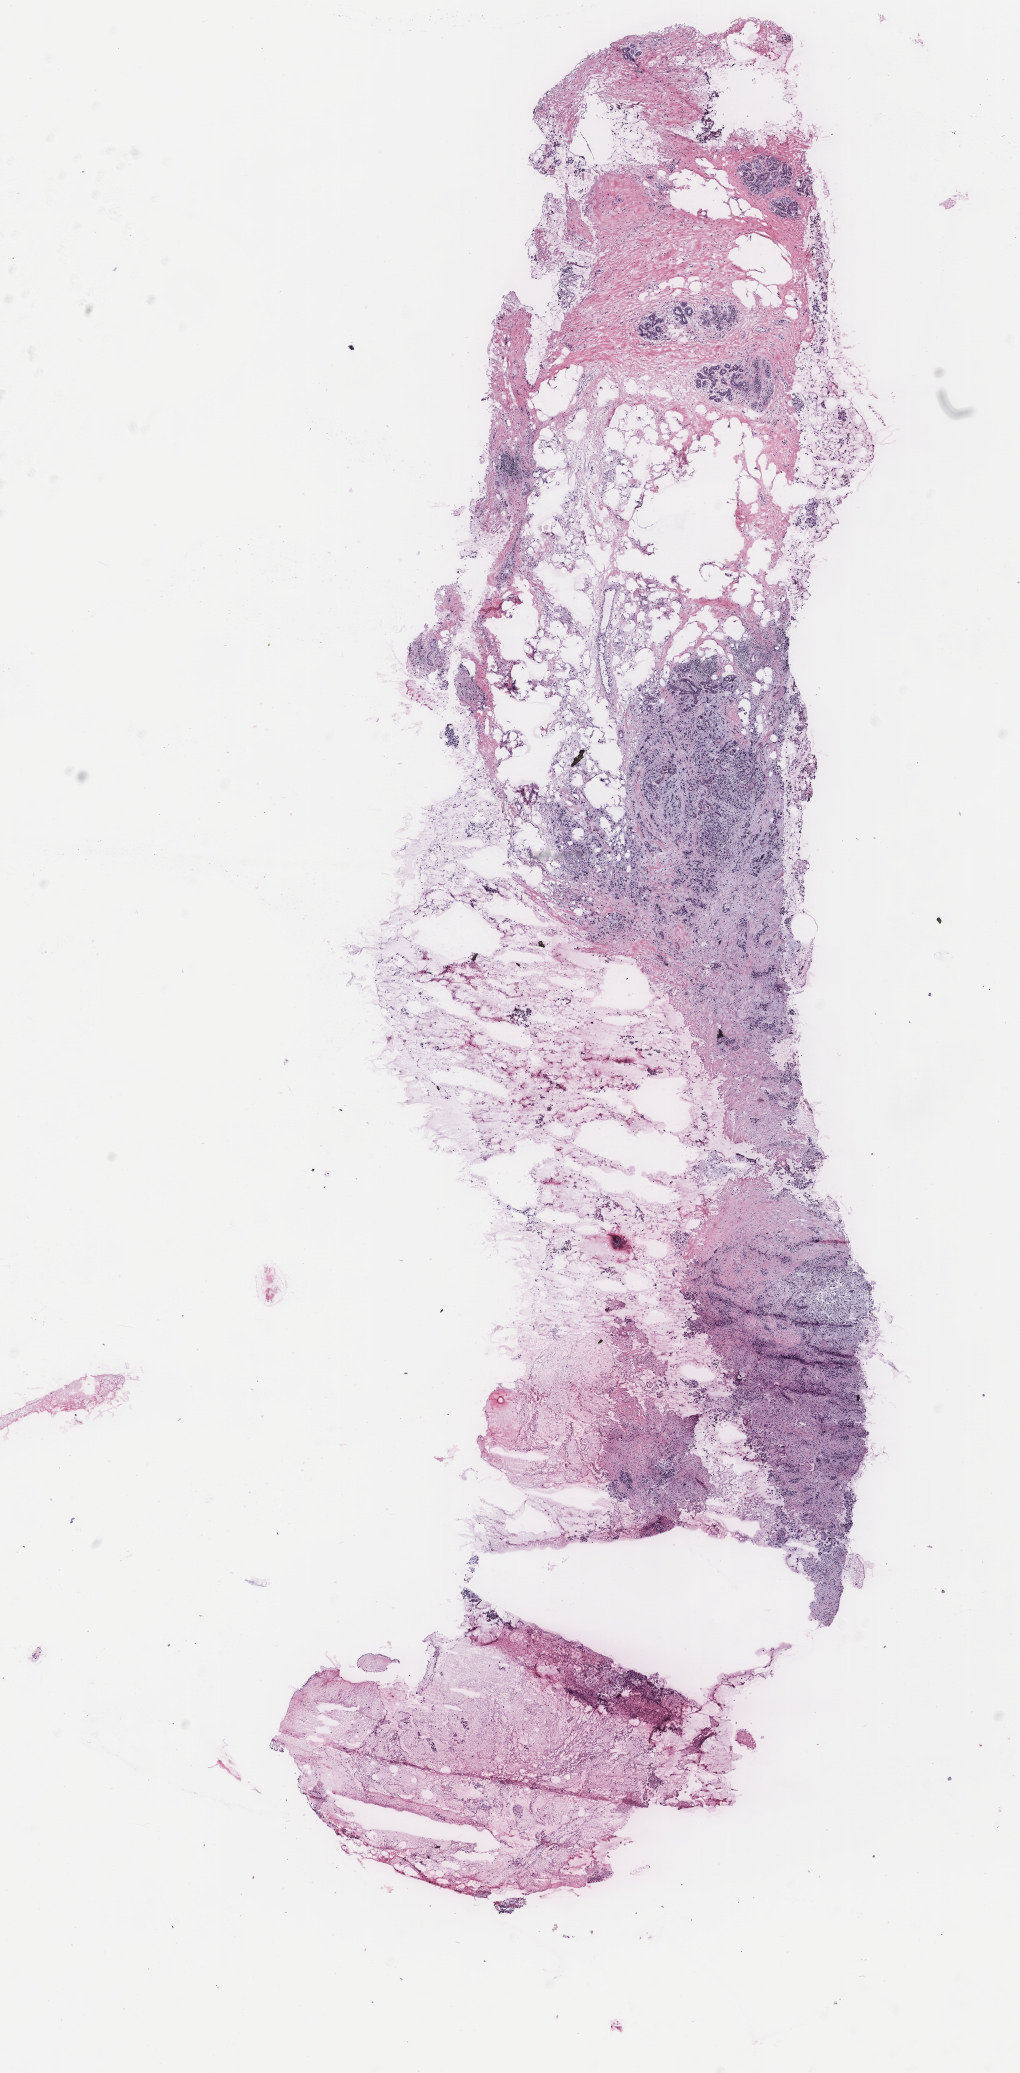
Whole-slide histology image, H&E-stained — whole scanned area (about 8.2 x 16.6 mm) shown as a low-resolution overview. 48-year-old female patient.
Specimen: tumour tissue sample, breast.